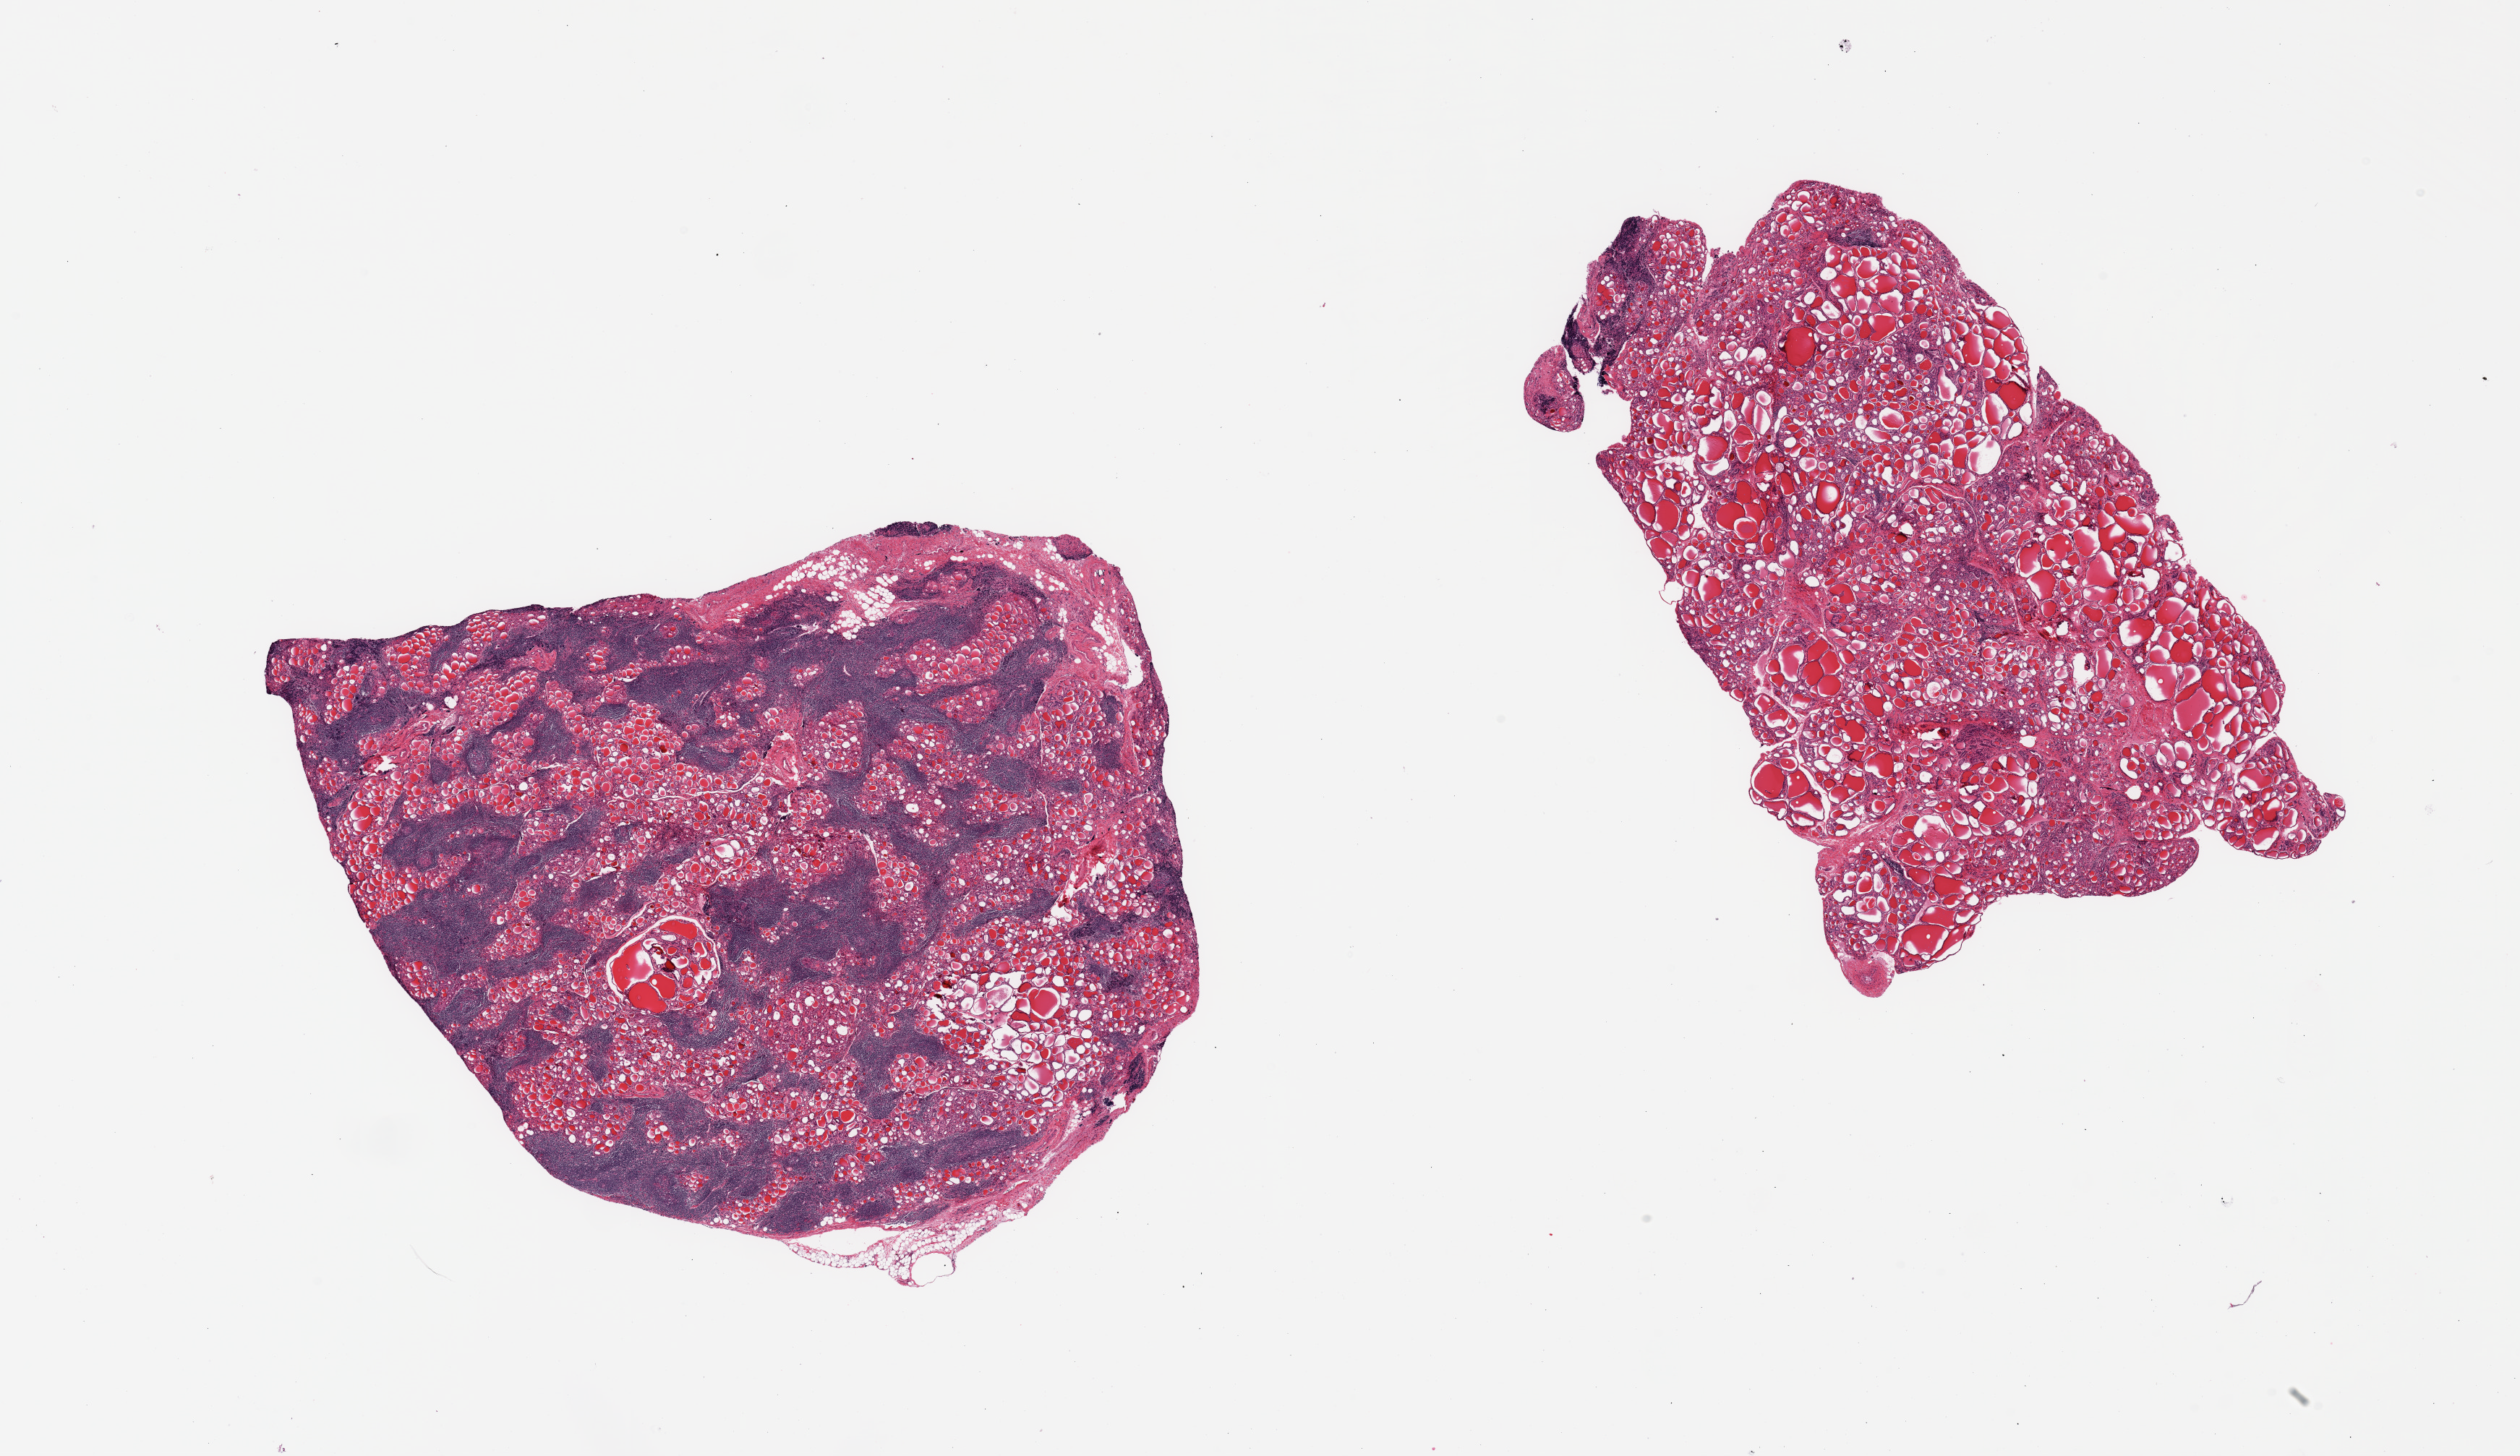
Digitized H&E-stained section, whole scanned area (about 27.6 x 15.9 mm) shown as a low-resolution overview; PAXgene-fixed paraffin-embedded (PFPE) section; sampled site (target tissue): thyroid; donor tissue sample. Female donor.
Reviewer comment on this tissue sample: 2 pieces; one shows diffuse interstitial lymphoid infiltration with germinal centers; the second shows interstitial fibrosis with micro nodularity, variable size of follicles and interstitial lymphoid infiltrate; Hashimoto disease (lymphocytic thyroiditis).